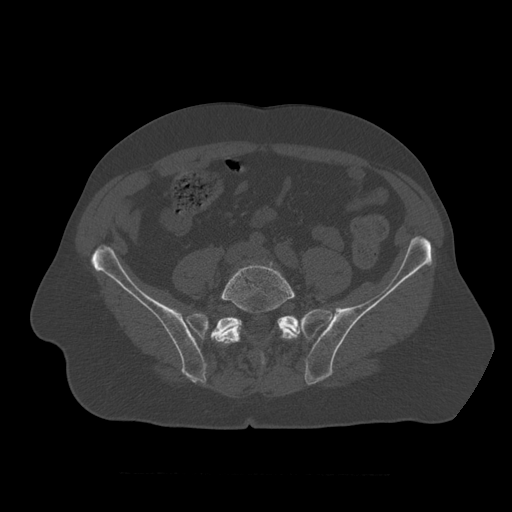
CT including the spine, one axial slice; position 249 of 450 along the scan axis; 120 kVp; bone window (W 1800 / L 400 HU); 512 × 512 image matrix. Patient age 75 years. Case-level facts recorded for this patient, not image findings: primary cancer: prostate.
Annotated regions visible in this slice (semi-automatic segmentation, software-assisted and operator-edited):
- L5 vertebra: bounding box <216,261,299,366> (left, top, right, bottom; pixels)